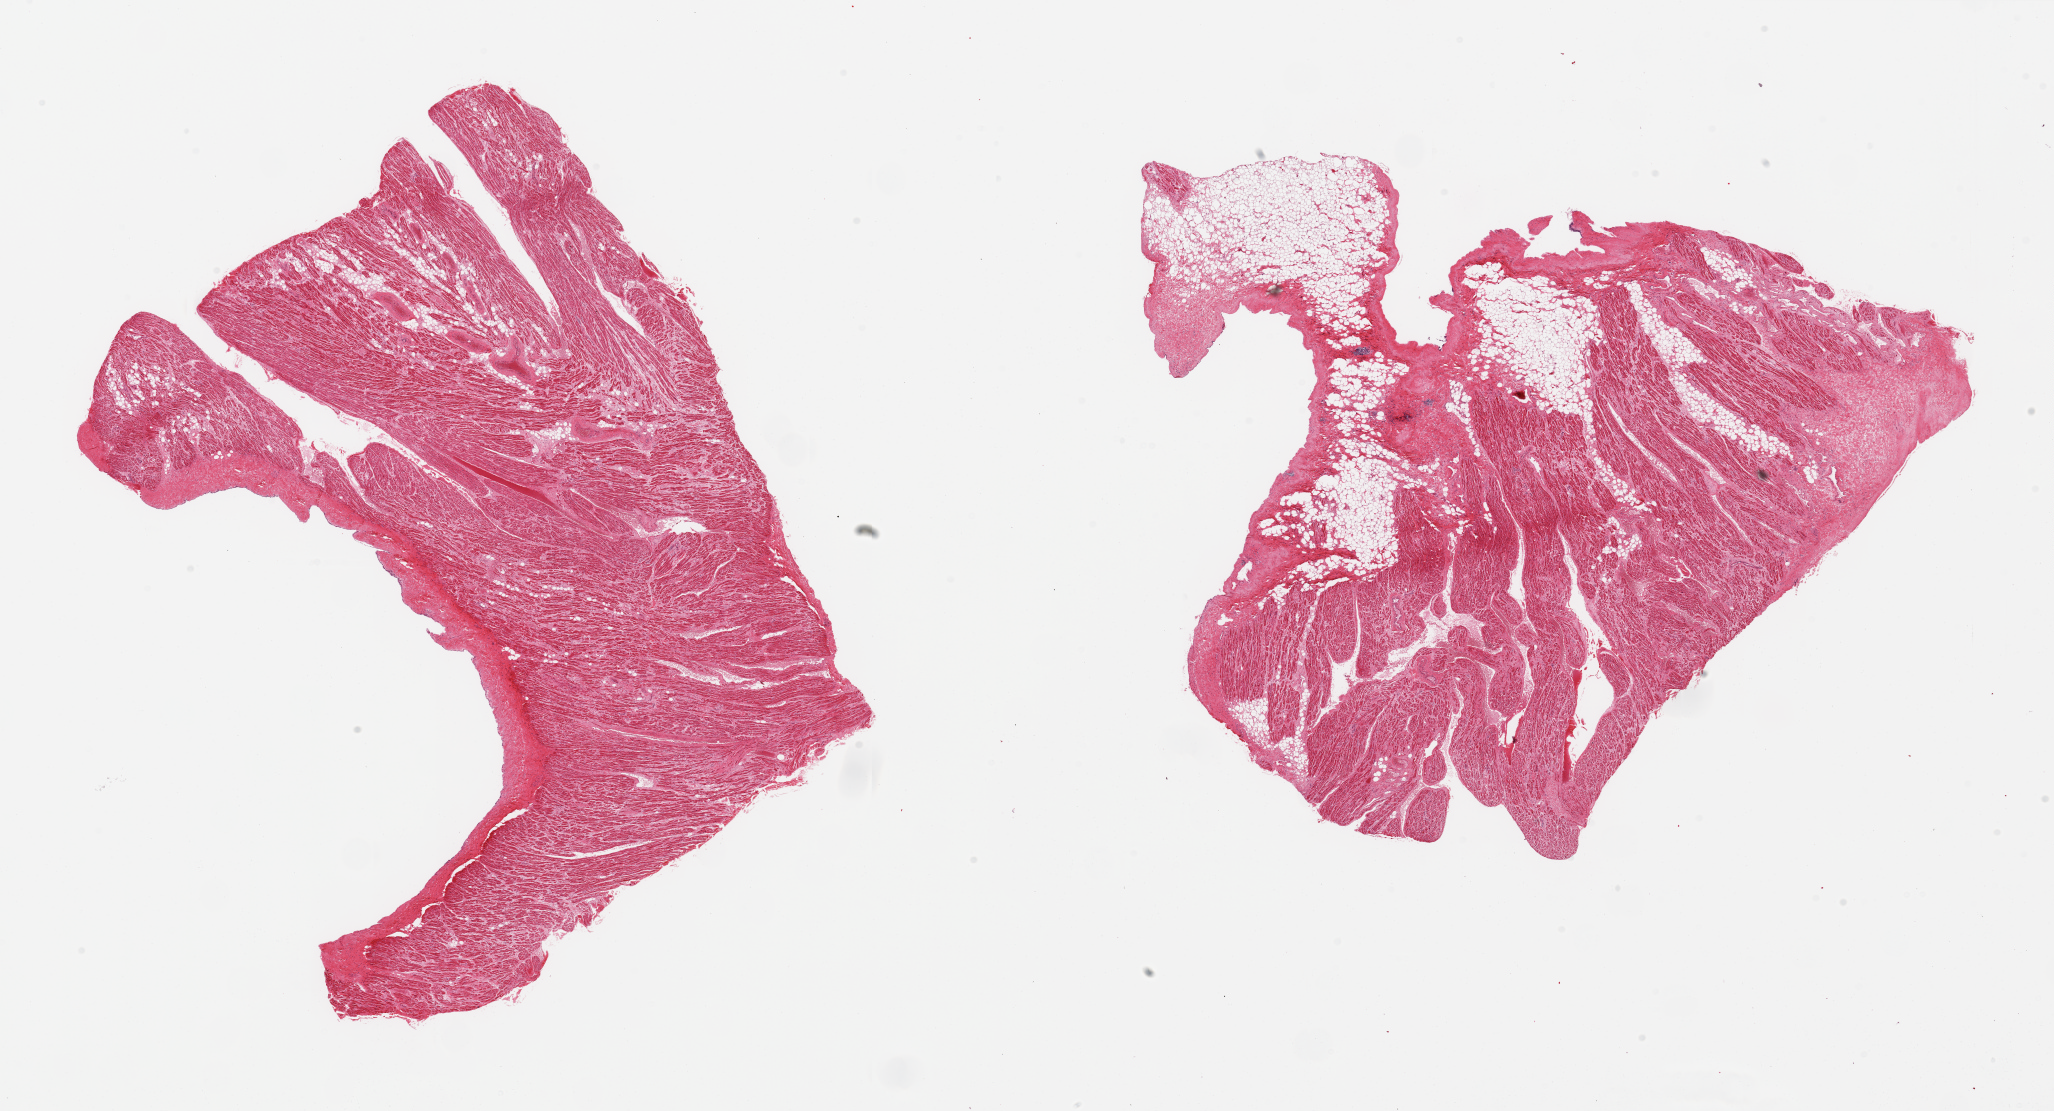
Haematoxylin and eosin whole-slide image, brightfield, whole scanned area (about 32.5 x 17.6 mm) shown as a low-resolution overview, PAXgene-fixed paraffin-embedded (PFPE) section, sampled site (target tissue): auricular appendage, tissue donor sample. Male donor.
Review note (as recorded): 2 pieces; 1 with 40% external & internal fat; other with 5% internal fat.